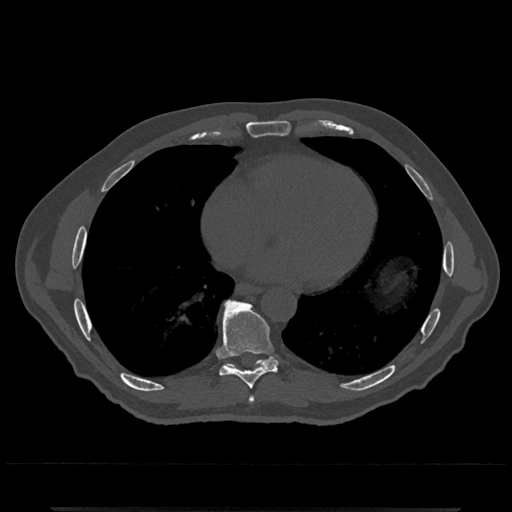
CT including the spine, one axial slice. Slice 658 of 797 in the series (ordered by position). 120 kVp. Bone window (W 1800 / L 400 HU). 0.5 mm slice thickness. 512 × 512 image matrix, field of view 393 × 393 mm. Patient: male, 67 years. Case-level facts recorded for this patient, not image findings: primary cancer: prostate.
Annotated regions visible in this slice (semi-automatically segmented with operator editing):
- T7 vertebra: bounding box (x1, y1, x2, y2) in pixels: (248, 396, 254, 404)
- T8 vertebra: (217, 299, 279, 389)
- T9 vertebra: (219, 301, 278, 369)